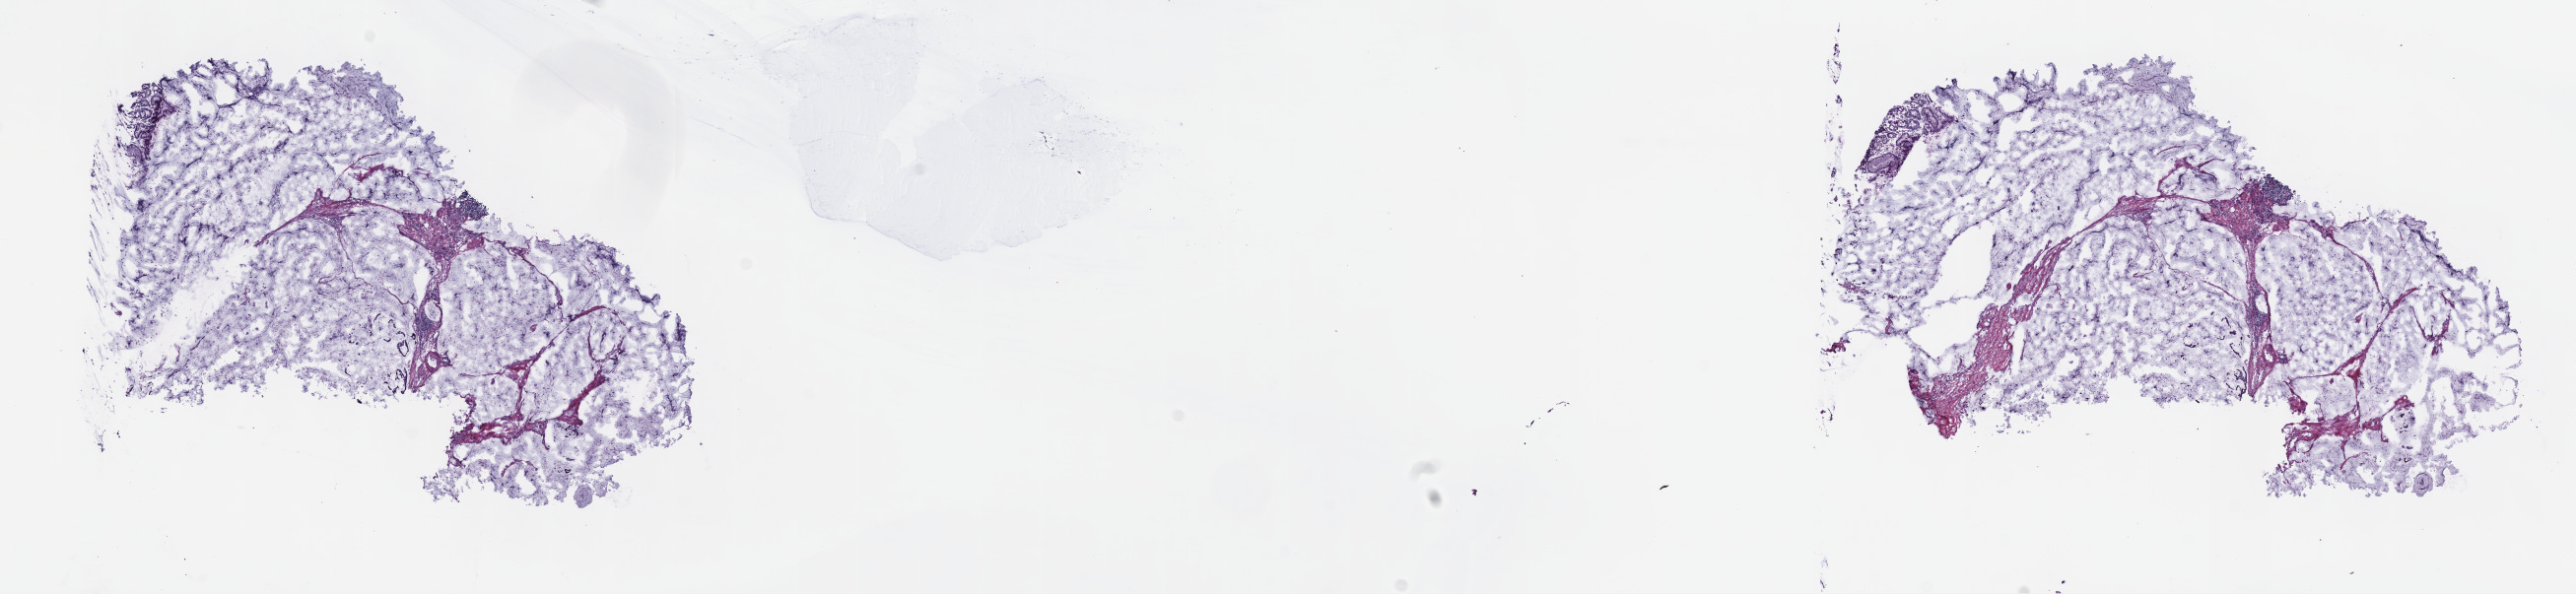
Whole-slide histology image, Hematoxylin and eosin (H&E) stained — shown as a low-resolution overview of the whole scanned area (about 21.1 x 4.9 mm, from a 40x scan), frozen section from the top of the tissue portion, stomach, primary tumour sample. Male, age 68 years at initial diagnosis. Histologic grade: G1 (well differentiated). Pathologist review of this section (percent, as recorded): tumour cells 80%, tumour nuclei 80%, normal cells 0%, stromal cells 20%, necrosis 0%. Infiltration values recorded for this section: lymphocyte infiltration 60%, monocyte infiltration 20%, neutrophil infiltration 10%.
- pathologic diagnosis: Signet ring cell carcinoma
- TNM: T2 N0 M0
- AJCC pathologic stage: IB